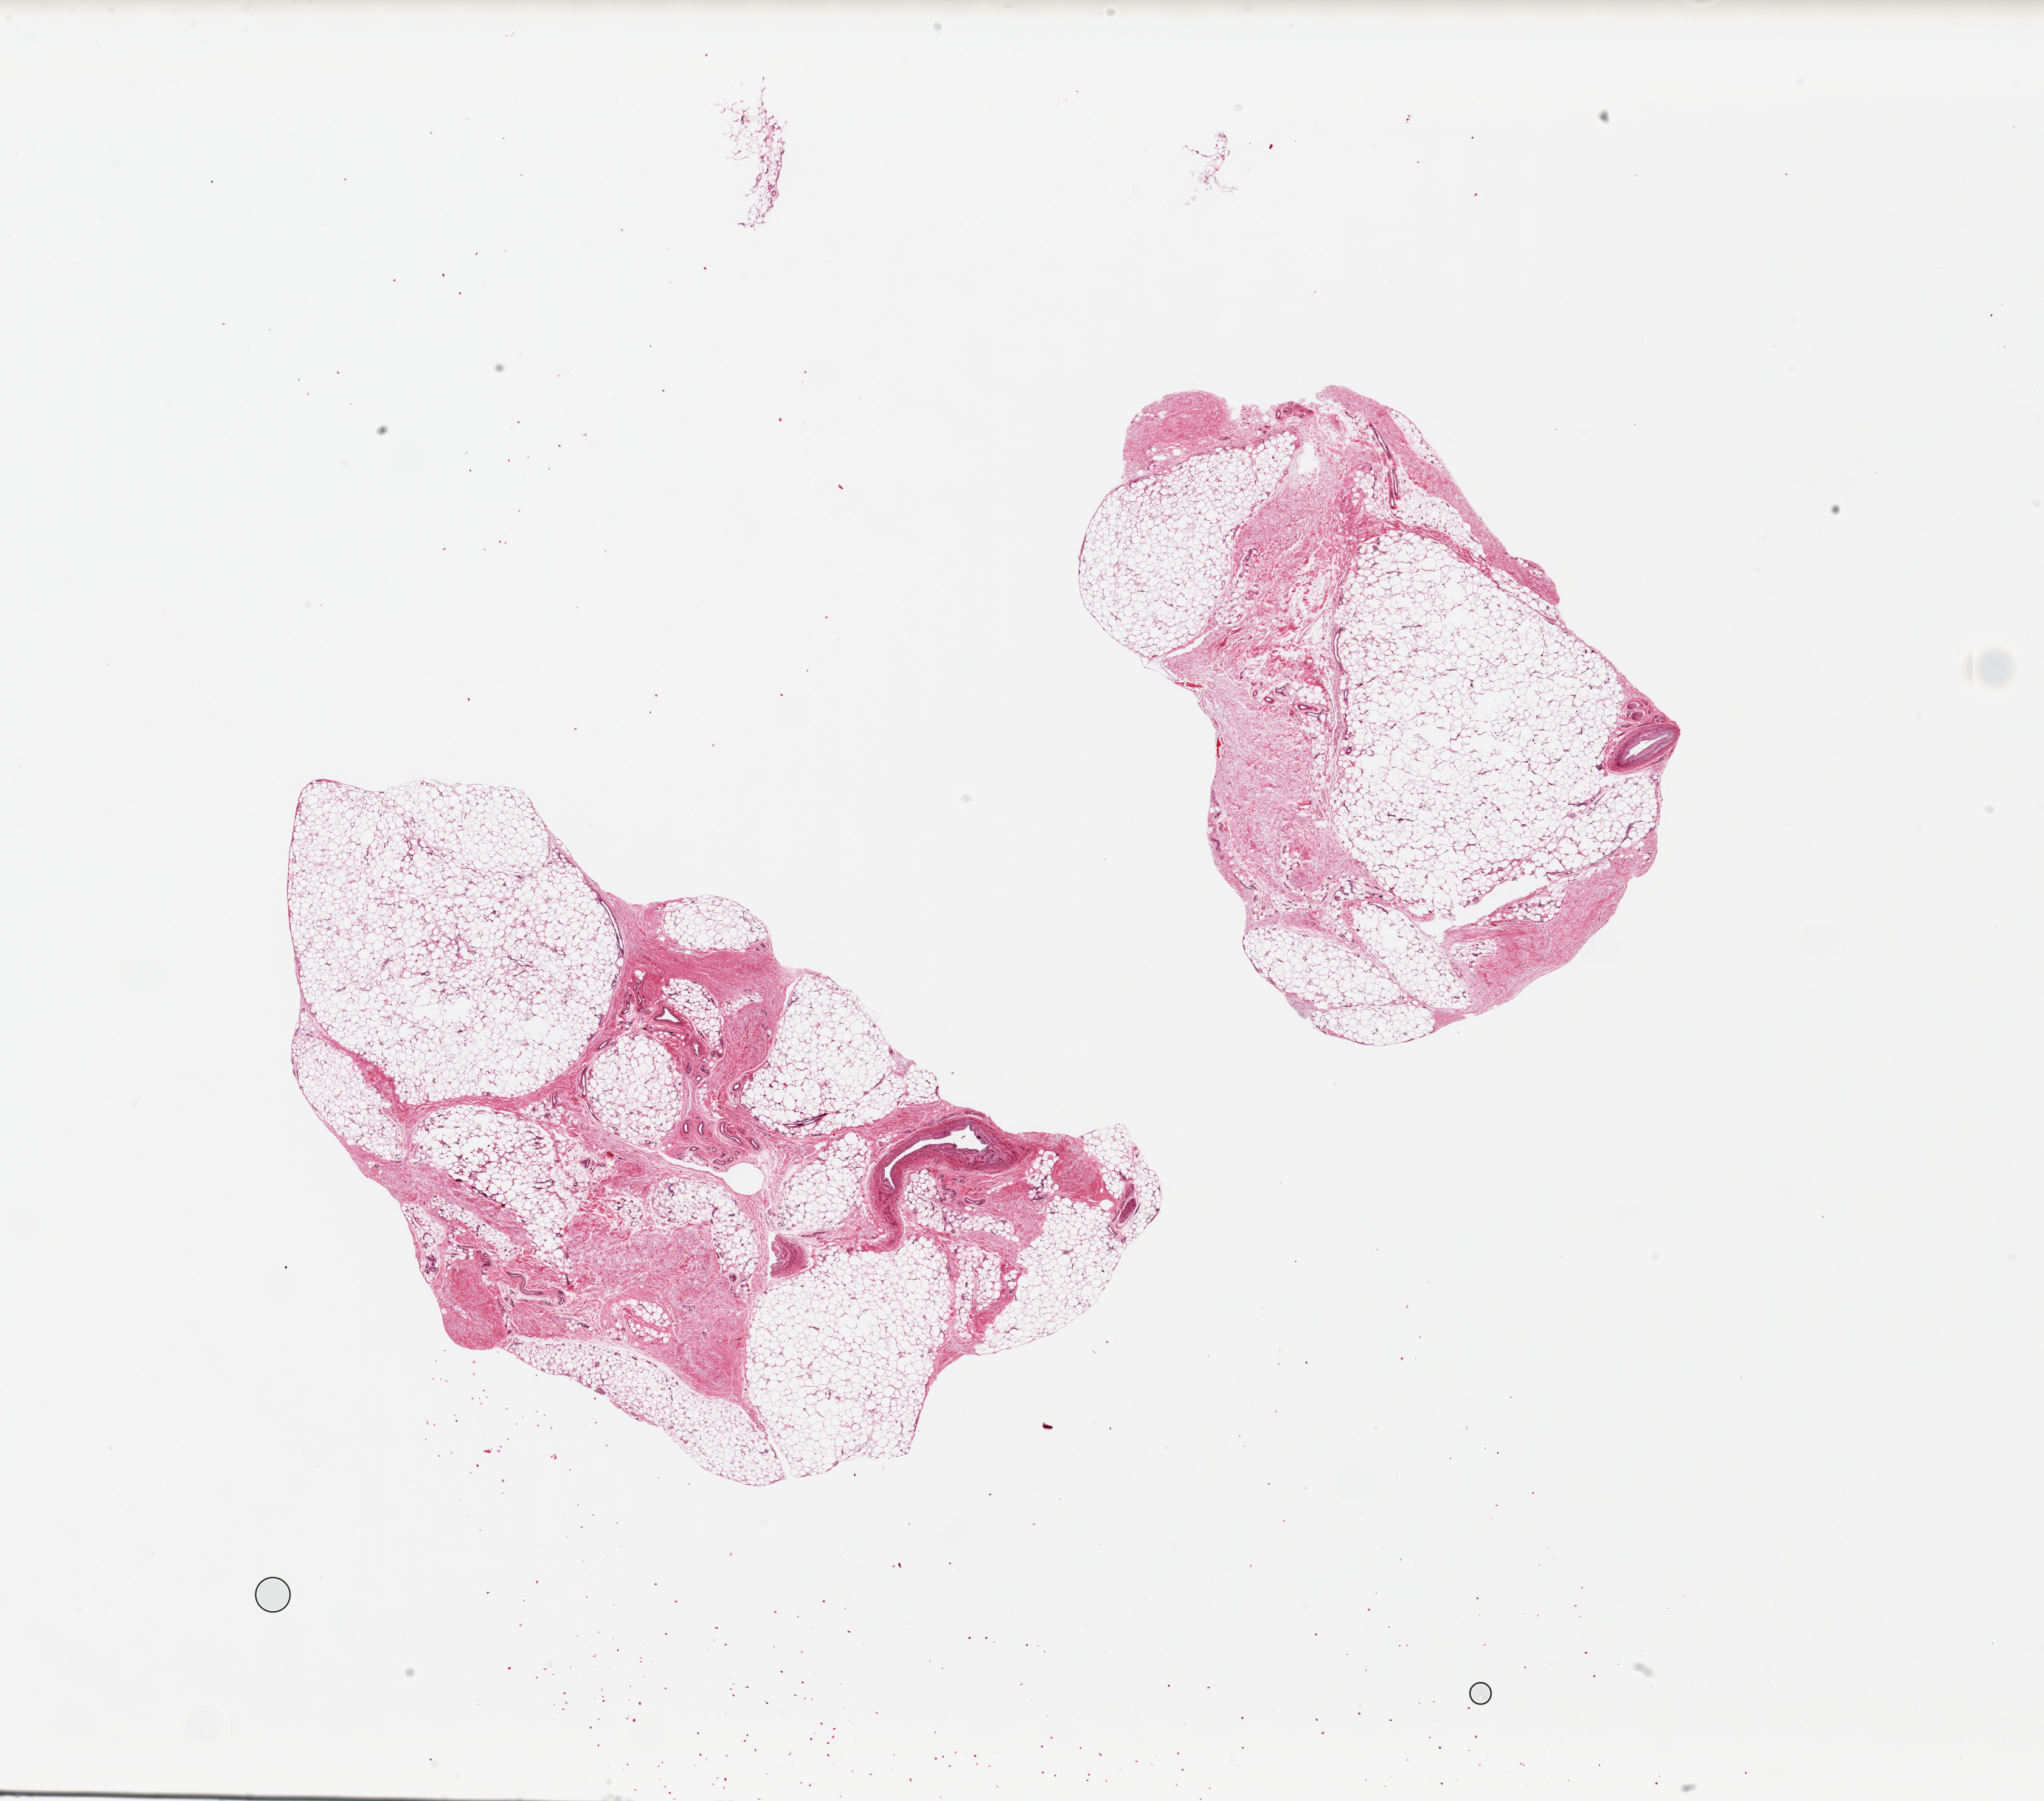
Hematoxylin and eosin (H&E) whole-slide image — low-resolution overview of the scanned area, about 26.6 x 23.4 mm (slide scanned at 20x); PAXgene-fixed, paraffin-embedded tissue; sampled site (target tissue): adipose tissue; tissue donor sample. Female donor.
Review note (as recorded): 2 pieces, 8x6 & 12x6mm; ~20% fibrous stroma separates adipose into lobules.